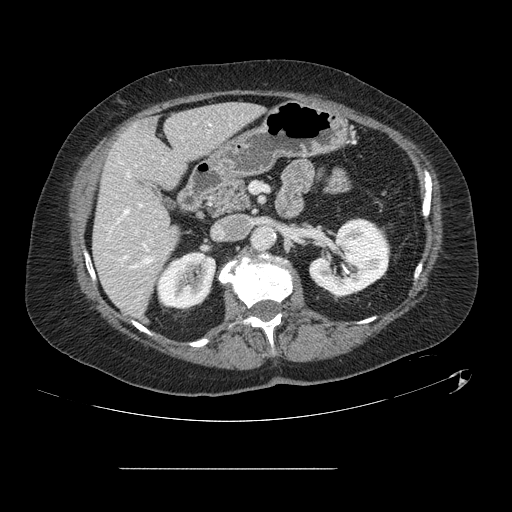
Contrast-enhanced abdominal CT, one axial slice. Slice 56 of 148 in the series (ordered by position). 120 kVp. Soft-tissue window (W 400 / L 40 HU). 2.5 mm slice thickness. 512 × 512 image matrix. Female patient, age 75 years. Case-level facts recorded for this patient, not image findings: diagnosis: colorectal cancer liver metastases, imaged before liver resection; multiple liver metastases: no; largest metastasis: 2.4 cm; disease in both lobes: no.
Outlined on this slice (outlined manually by an expert reader):
- hepatic veins: bounding box (x1, y1, x2, y2) in pixels: (124, 173, 152, 268)
- liver: (94, 105, 261, 317)
- planned liver remnant (the part of the liver to remain after resection): (94, 105, 261, 317)
- portal vein (with intrahepatic branches): (124, 204, 142, 258)